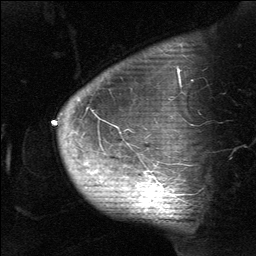
Breast MRI (dynamic contrast-enhanced), one sagittal slice; position 50 of 64 along the scan axis; dynamic contrast-enhanced study with each time point stored as its own series, time point 2 of 3 at this slice position (early post-contrast, ordered by acquisition time); 1.5 T; TE 4.8 ms, TR 27 ms; 2 mm slice thickness; 256 × 256 image matrix, field of view 180 × 180 mm. Patient: female, 39 years. Case-level facts recorded for this patient, not image findings: setting: breast cancer imaged before/during neoadjuvant chemotherapy; receptor status: HER2-positive.
Structures marked on this image (semi-automatically segmented with operator editing):
- analysis volume of interest (the breast-tissue region the enhancement analysis was run in; not a lesion): bounding box (x1, y1, x2, y2) in pixels: (58, 40, 201, 217)
- tumour enhancement mask (voxels above the 90 % enhancement threshold inside the analysis volume of interest): (143, 70, 179, 206)